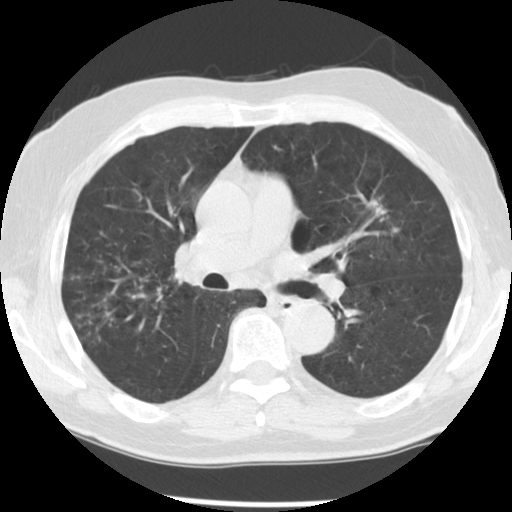
Low-dose screening chest CT, axial slice, third screening round (two years after baseline), lung window (W 1500 / L -600 HU), standard (soft-tissue) reconstruction kernel (STANDARD), slice 74 of 131 in the series, 512 × 512 image matrix, field of view 330 × 330 mm. Male participant, aged 70 years at enrolment.
• Expert reader's lesion annotation, box from (x=356, y=185) to (x=410, y=241) px.
• The screening reader recorded 3 non-calcified nodules or masses ≥4 mm on this exam (left upper lobe, left upper lobe, right lower lobe); which of them this box marks is not recorded.
• Lung cancer was diagnosed 74 days after this screen: adenocarcinoma, NOS, left upper lobe, moderately differentiated (G2), stage IIIA (AJCC 6th edition), 17 mm at pathology.